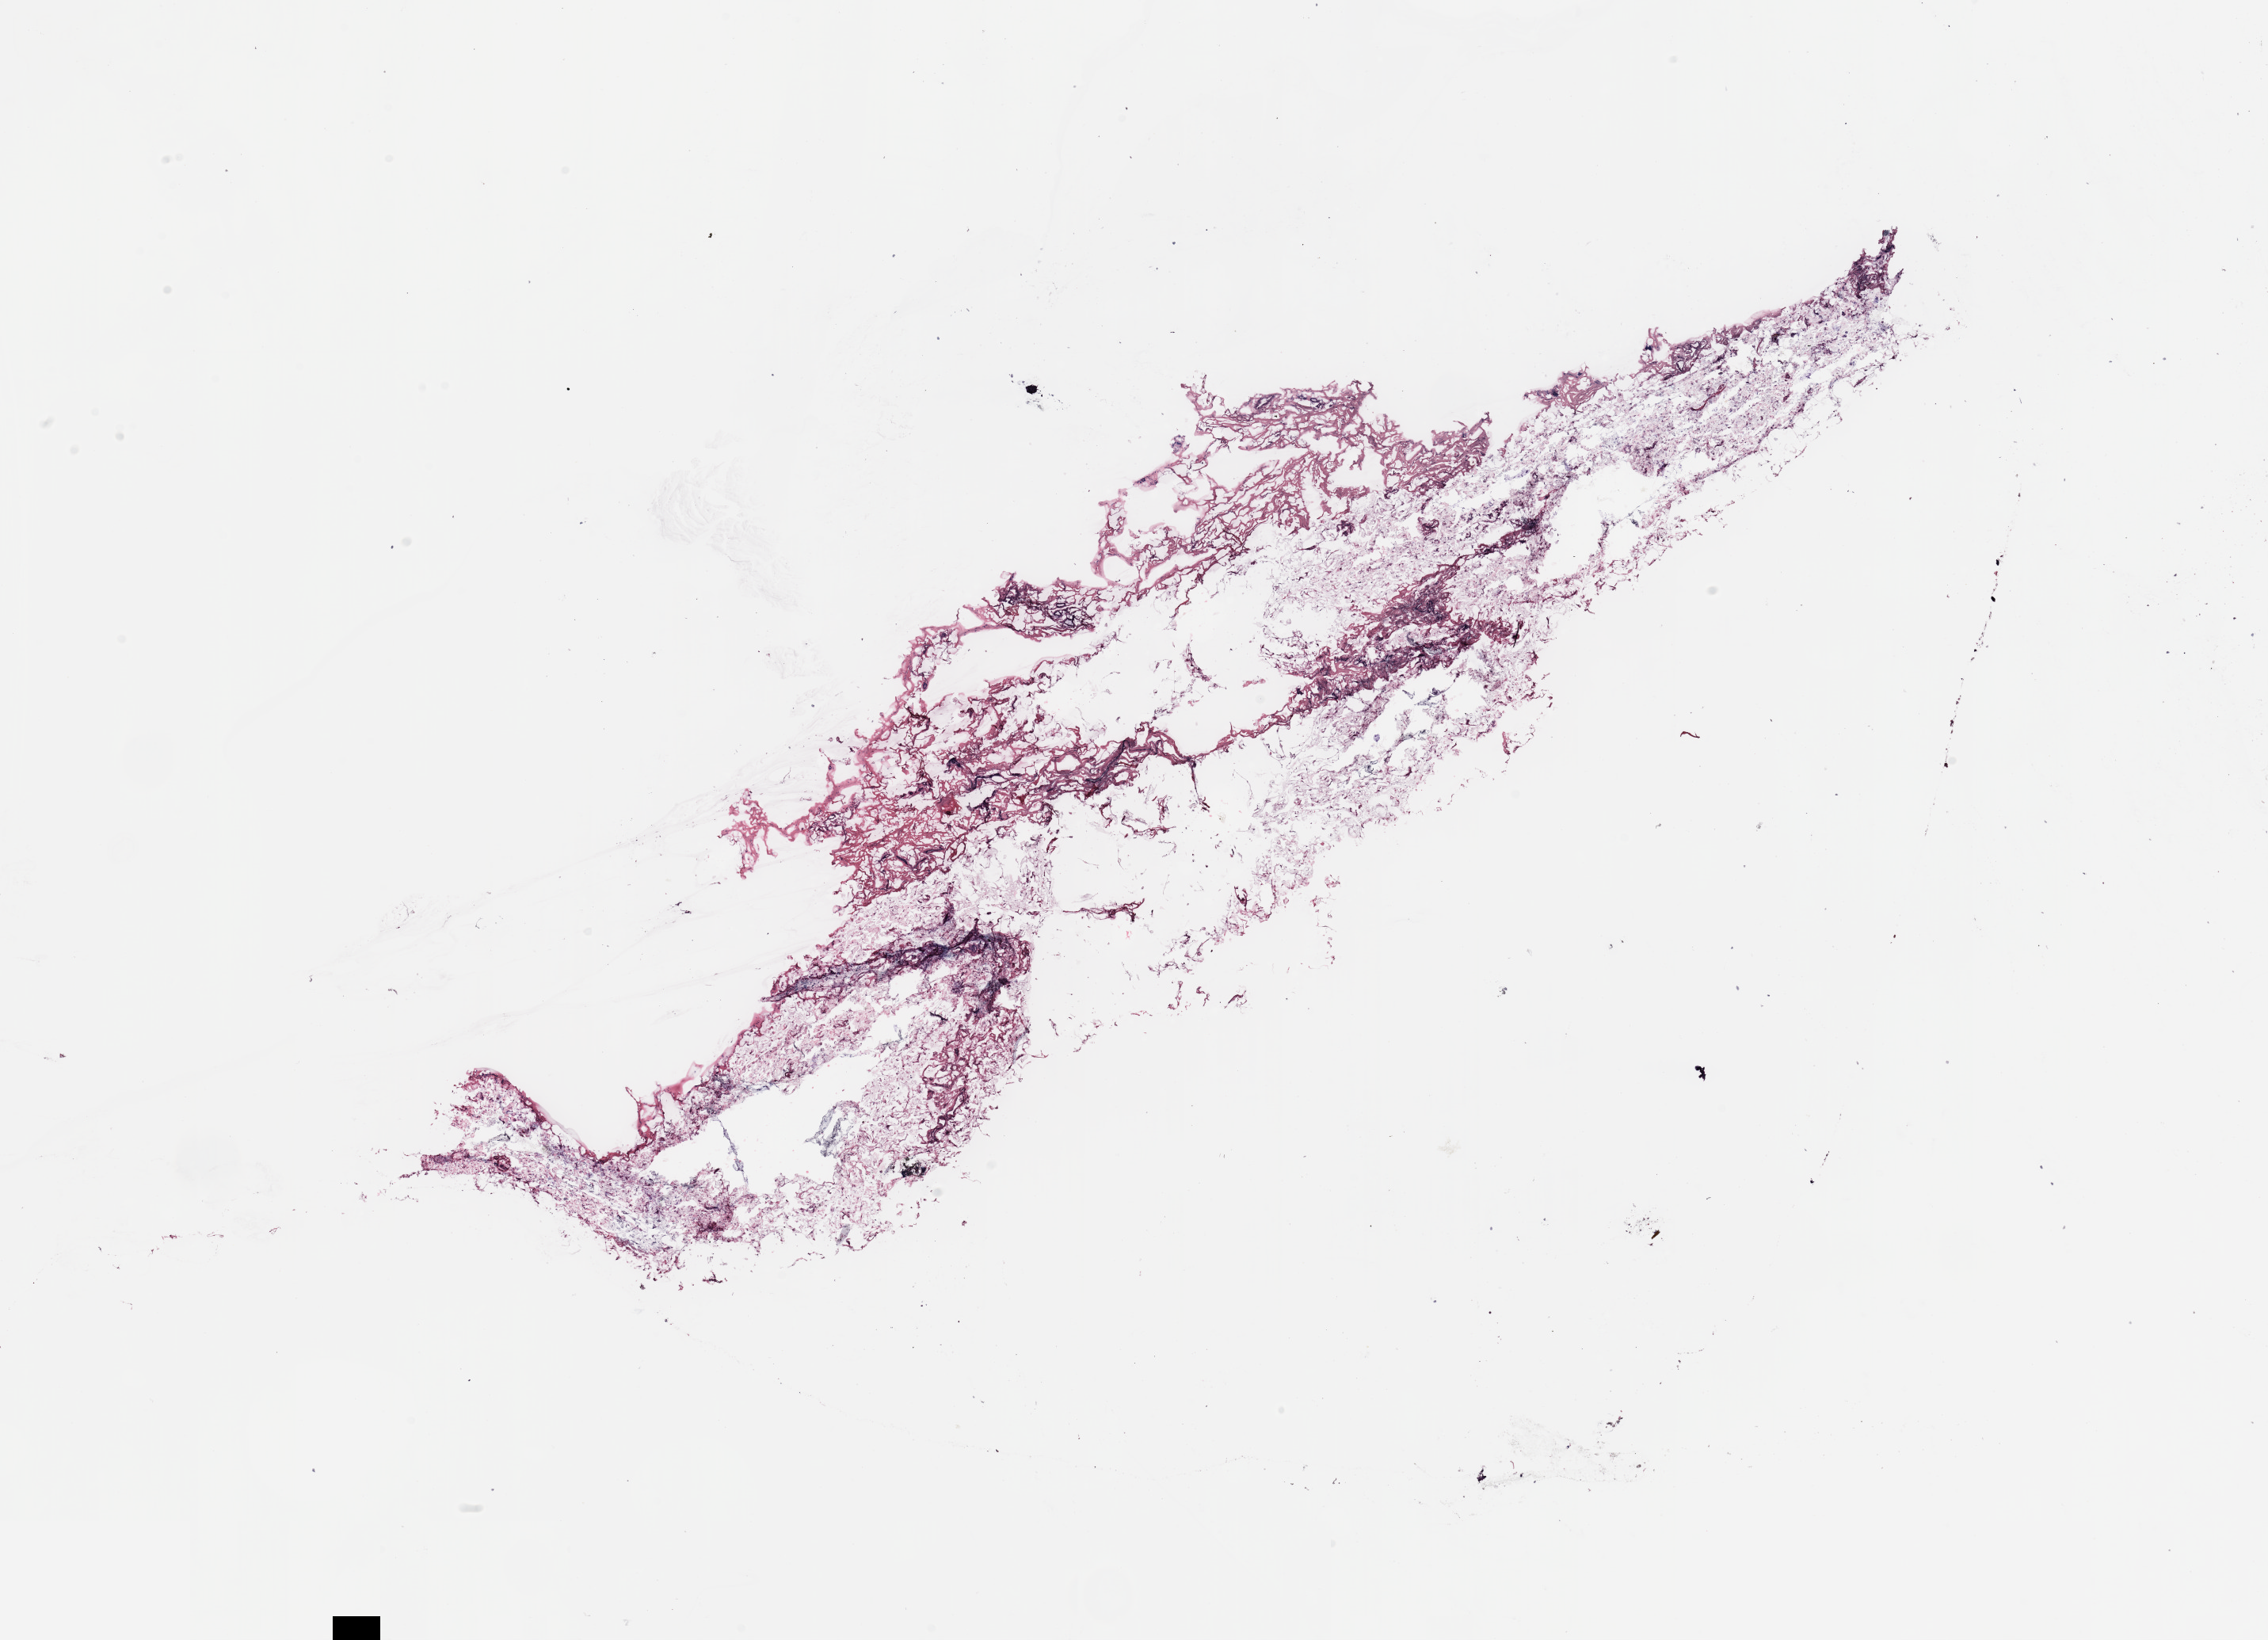
Whole-slide histology image, Hematoxylin and eosin (H&E) stained, a low-resolution overview of the entire scanned area, about 22.6 x 16.4 mm. Breast, tumour tissue. 65-year-old female patient.
* AJCC pathologic stage: IIA
* diagnosis: Infiltrating duct carcinoma, NOS